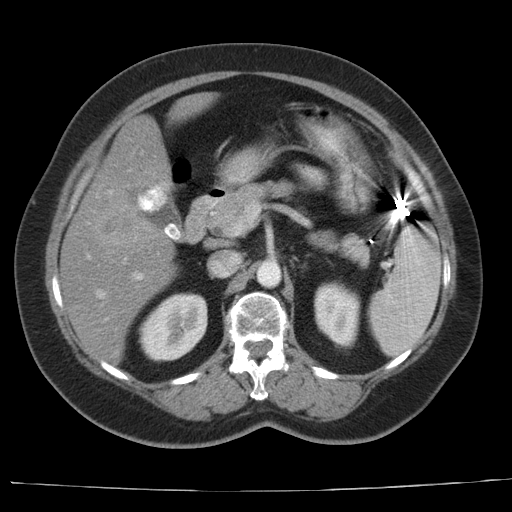
Contrast-enhanced abdominal CT, one axial slice; slice 16 of 44 in the series (ordered by position); intravenous contrast given; soft-tissue window (W 400 / L 40 HU); 5 mm slice thickness; 512 × 512 image matrix, field of view 373 × 373 mm. Female patient. Case-level facts recorded for this patient, not image findings: diagnosis: colorectal cancer liver metastases, imaged before liver resection.
Annotated regions visible in this slice (expert manual segmentation):
- hepatic veins: box from (x=97, y=191) to (x=112, y=298) px
- liver: (x=60, y=96)–(x=212, y=364)
- planned liver remnant (the part of the liver to remain after resection): (x=105, y=95)–(x=214, y=188)
- portal vein (with intrahepatic branches): (x=133, y=152)–(x=143, y=280)
- liver metastasis: (x=91, y=197)–(x=157, y=245)